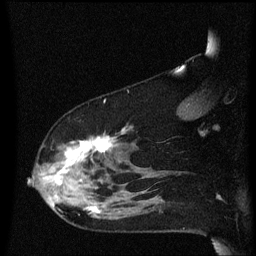
Breast MRI (dynamic contrast-enhanced), one sagittal slice. Slice 45 of 60 in the series (ordered by position). Dynamic contrast-enhanced series, image 2 of 3 at this slice position (ordered by acquisition). 1.5 T. TE 4.2 ms, TR 8.4 ms. 256 × 256 image matrix, field of view 200 × 200 mm. Female patient, age 48 years.
Structures marked on this image (semi-automatic segmentation, software-assisted and operator-edited):
- analysis volume of interest (the breast-tissue region the enhancement analysis was run in; not a lesion): bounding box [x1, y1, x2, y2] px = [31, 128, 134, 221]
- tumour enhancement mask (voxels above the 70 % enhancement threshold inside the analysis volume of interest): [56, 136, 113, 213]